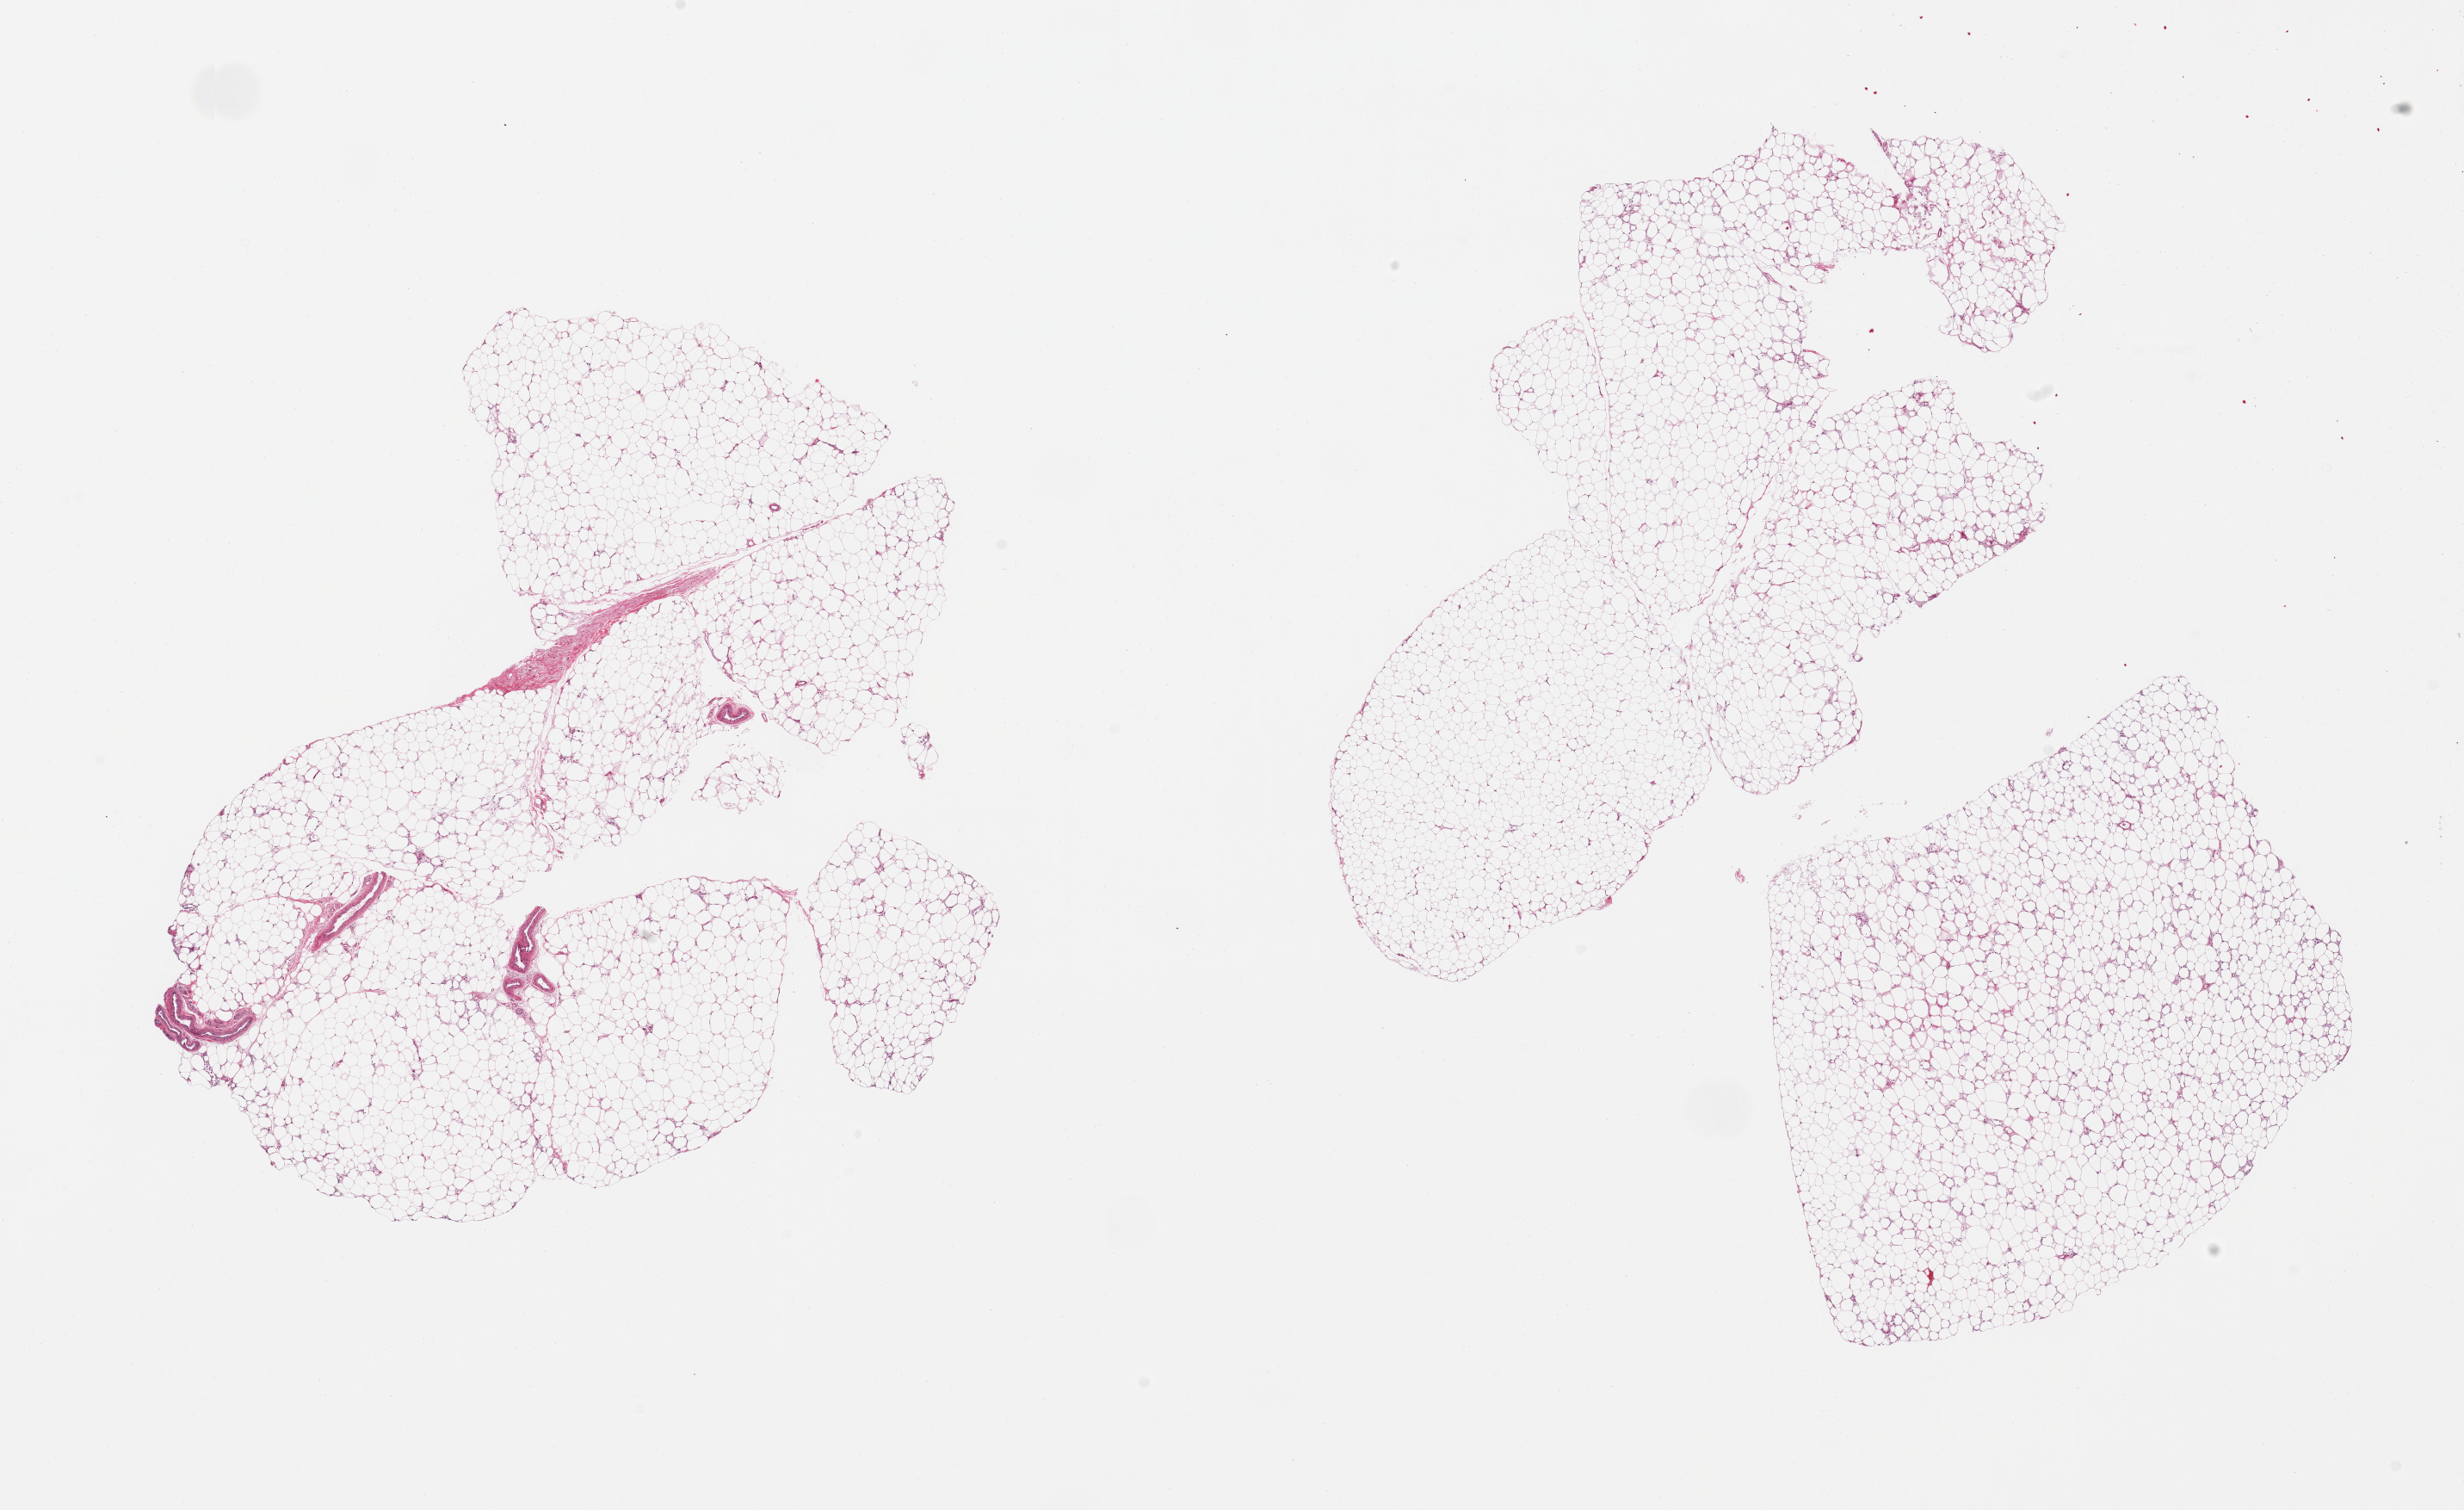
Digitized hematoxylin and eosin (H&E)-stained section — whole scanned area (about 22.6 x 13.9 mm) shown as a low-resolution overview. PAXgene-fixed, paraffin-embedded tissue. Section of adipose tissue (target tissue). Donor tissue sample. Female donor.
• reviewer comment on this tissue sample: 2 pieces